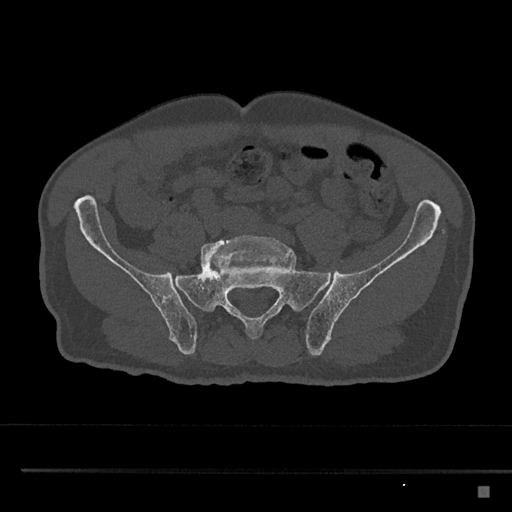
CT including the spine, one axial slice; slice 544 of 797 in the series (ordered by position); reconstruction kernel Br40s/3; 120 kVp; bone window (W 1800 / L 400 HU); 0.5 mm slice thickness; 512 × 512 image matrix, field of view 391 × 391 mm. Male patient, age 59 years. Case-level facts recorded for this patient, not image findings: primary cancer: prostate.
Outlined on this slice (semi-automatic segmentation, software-assisted and operator-edited):
- L5 vertebra: bounding box (x1, y1, x2, y2) in pixels: (201, 235, 292, 273)